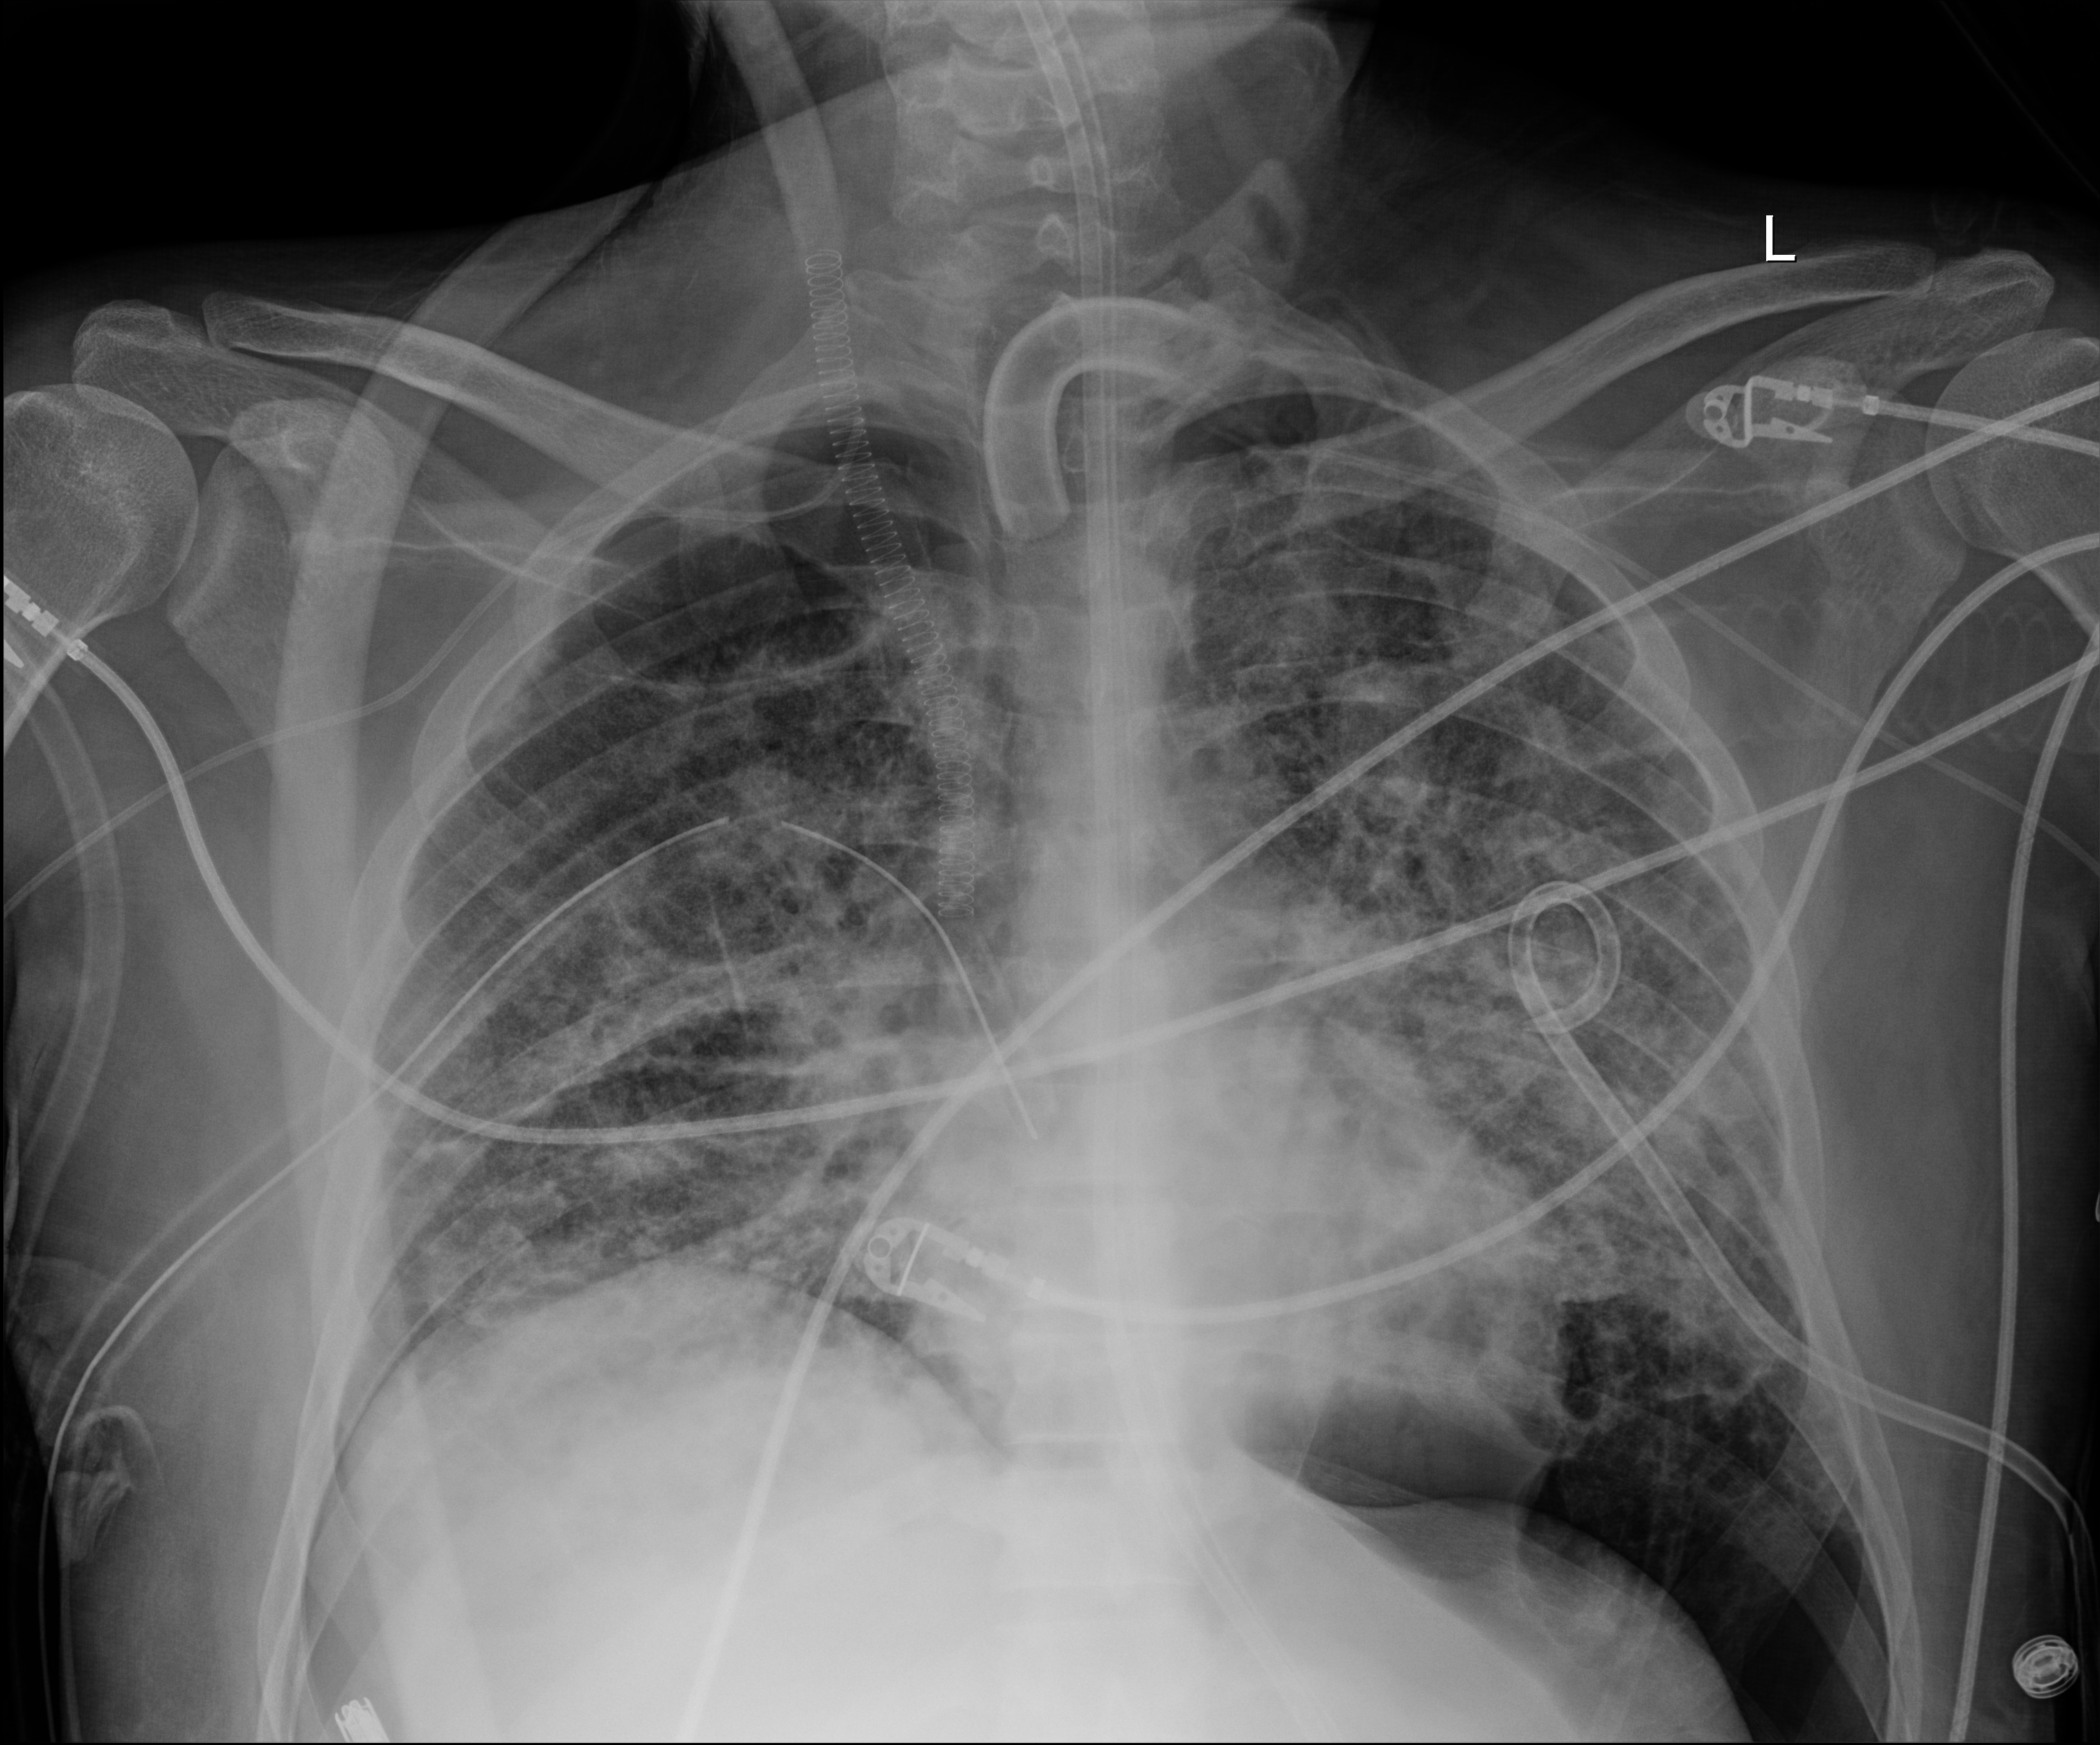
Chest radiograph (digital radiography); anteroposterior (AP) projection. Adult patient hospitalised with COVID-19, age 18–59 years.
From the hospital-stay record, not from the radiograph (when in the stay this image was taken is not recorded): mechanically ventilated during this hospital stay: yes; length of hospital stay: 60 days.